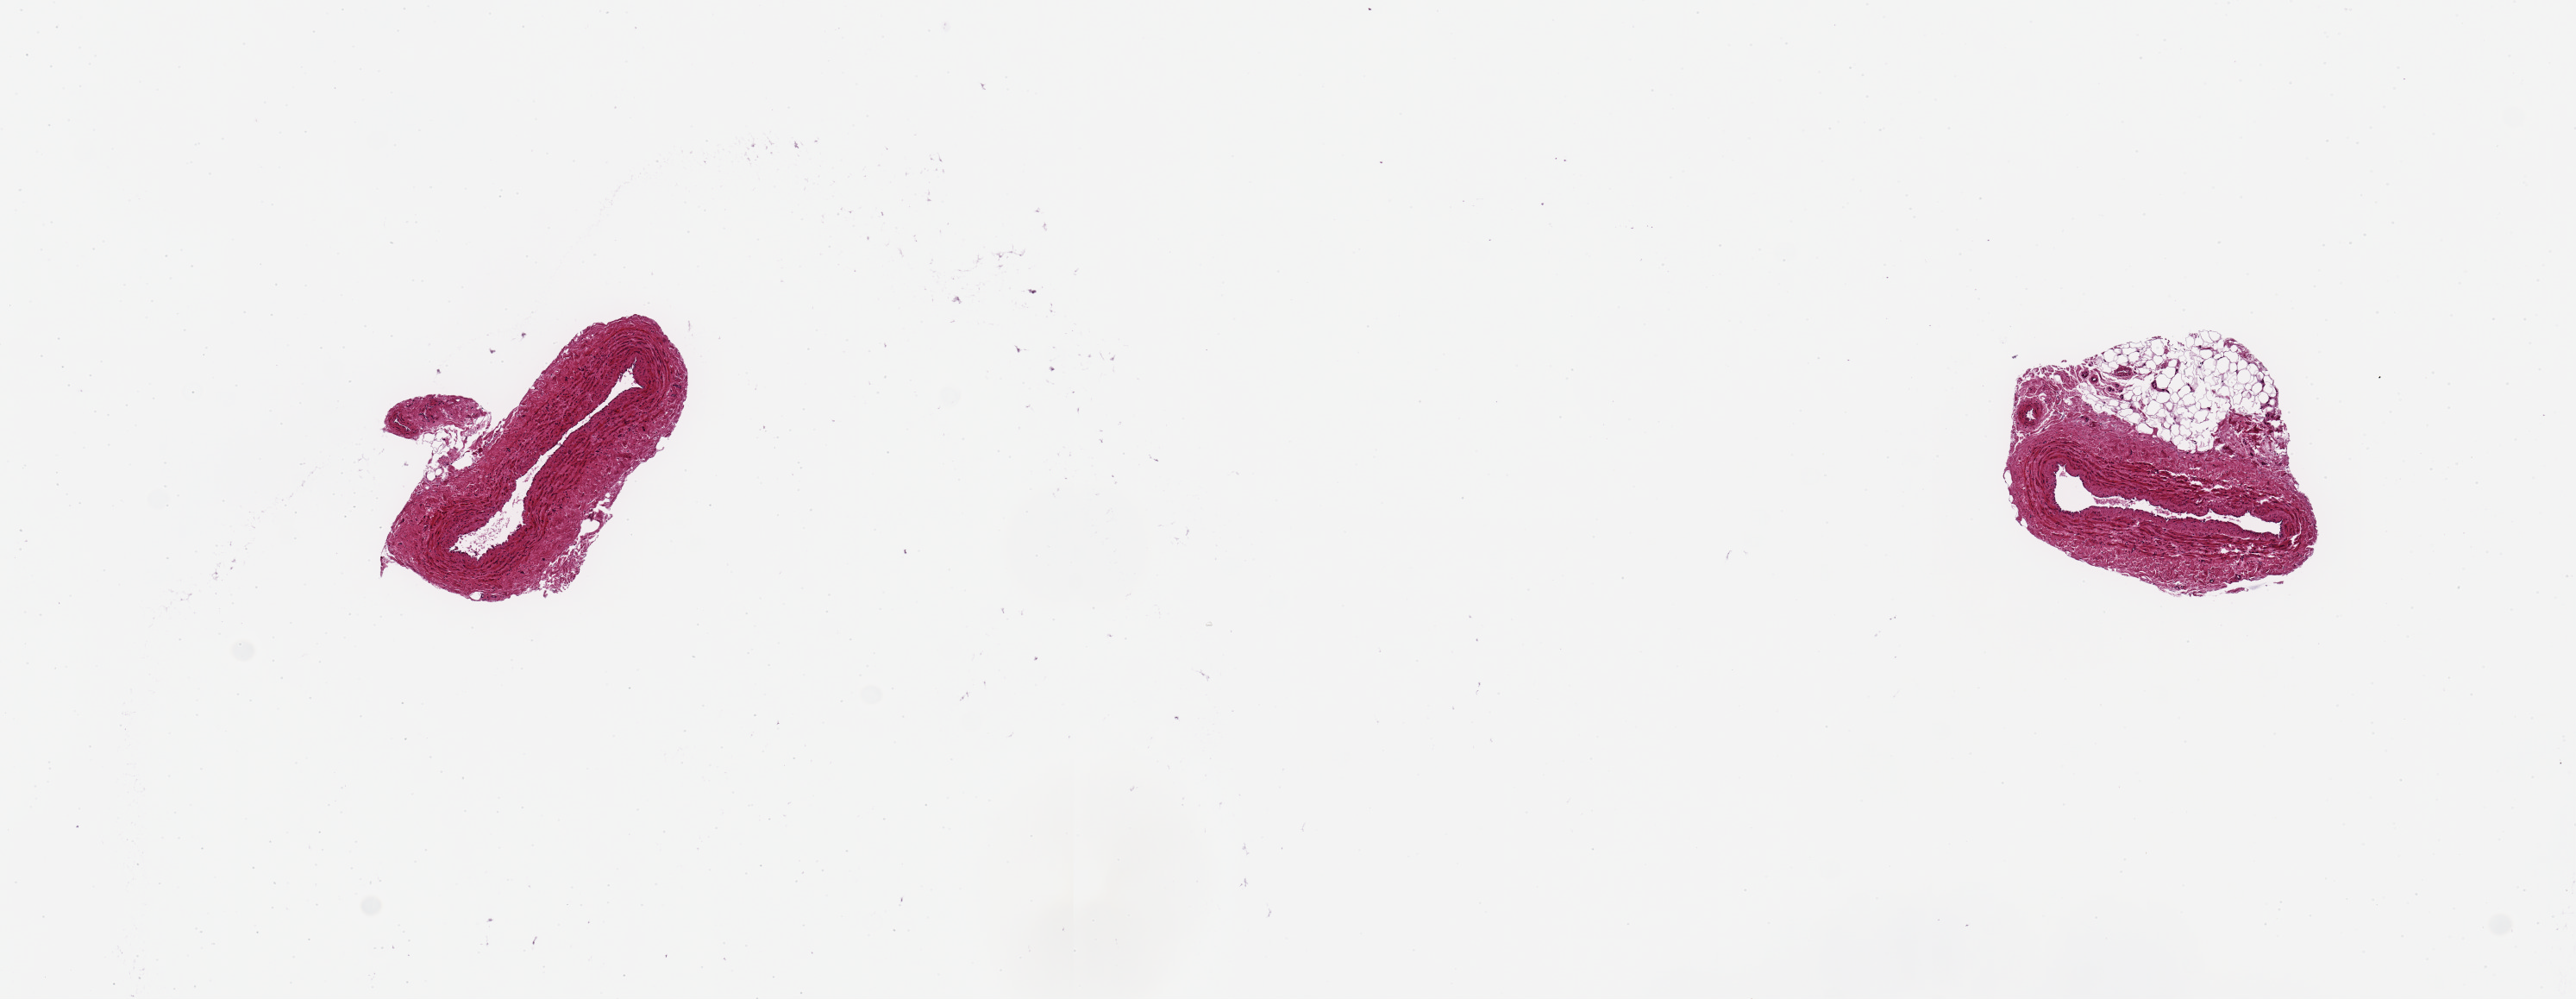
H&E whole-slide image — low-resolution overview of the scanned area, about 11.8 x 4.6 mm (from a 20x scan), PAXgene-fixed, paraffin-embedded tissue, section of tibial artery (target tissue), donor tissue sample.
Pathologist's review note for this sample: 2 ~1.5mm diameter sections.